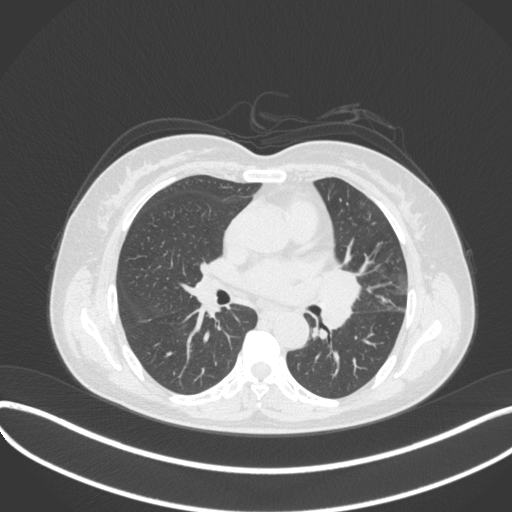
Chest CT, one axial slice. Position 188 of 373 along the scan axis. Reconstruction kernel B31f. 120 kVp. Lung window (W 1500 / L -600 HU). 512 × 512 image matrix. Female patient, age 54 years. From the clinical record (not read from this slice): clinical TNM (as recorded): T2a N1 M0.
Outlined on this slice (bounding box drawn by a radiologist):
- lung tumour (recorded histology: small cell carcinoma): bounding box <312,261,363,335> (left, top, right, bottom; pixels)